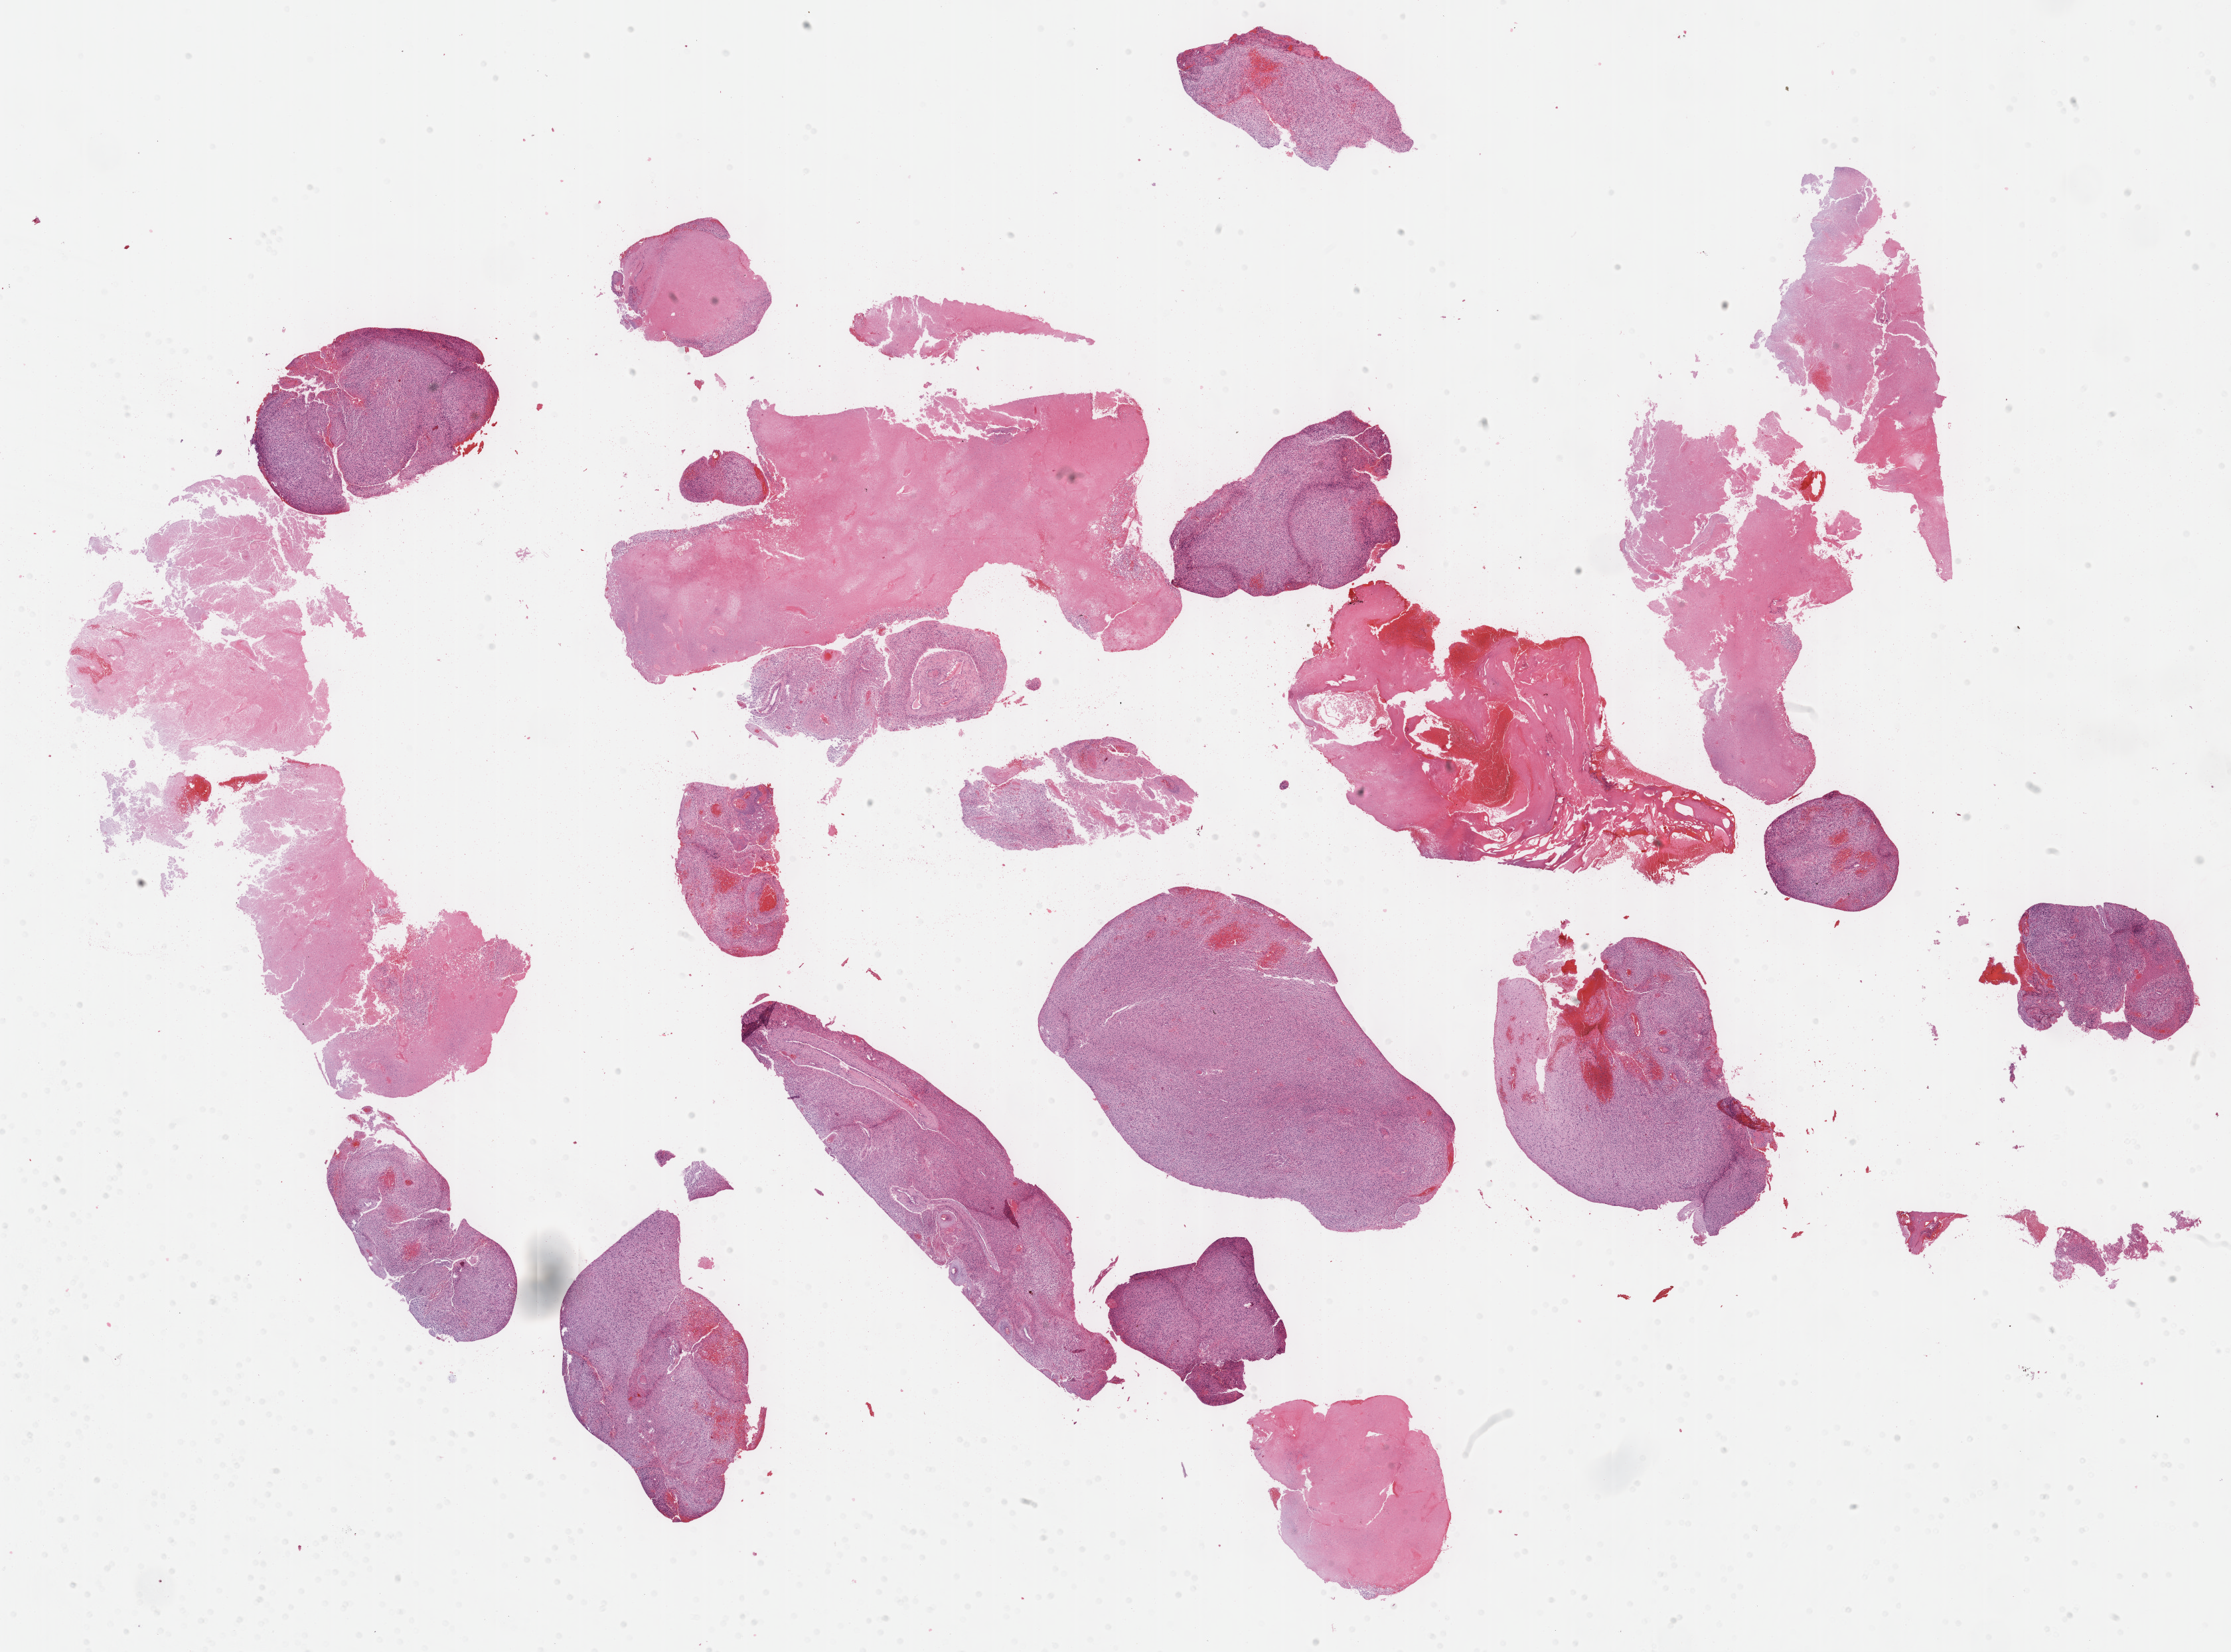
Digitized H&E tissue section (whole slide) — a low-resolution overview of the entire scanned area, about 27.2 x 20.1 mm, formalin-fixed paraffin-embedded (FFPE) diagnostic section, primary tumour sample from the brain. Female, age 65 years at initial diagnosis.
Pathologic diagnosis: Glioblastoma.